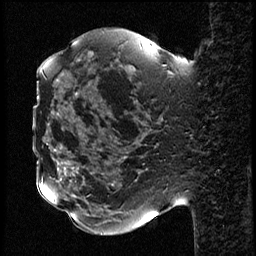
Breast MRI (dynamic contrast-enhanced), one sagittal slice. Position 23 of 78 along the scan axis. Dynamic contrast-enhanced study with each time point stored as its own series, time point 2 of 3 at this slice position (early post-contrast, ordered by acquisition time). 1.5 T. TE 4.2 ms, TR 17.6 ms. 256 × 256 image matrix, field of view 200 × 200 mm. Female patient, age 42 years. Case-level facts recorded for this patient, not image findings: setting: breast cancer imaged before/during neoadjuvant chemotherapy; receptor status: HER2-positive.
Outlined on this slice (semi-automatically segmented with operator editing):
- analysis volume of interest (the breast-tissue region the enhancement analysis was run in; not a lesion): bounding box [x1, y1, x2, y2] px = [50, 48, 131, 129]
- tumour enhancement mask (voxels above the 100 % enhancement threshold inside the analysis volume of interest): [129, 66, 131, 68]